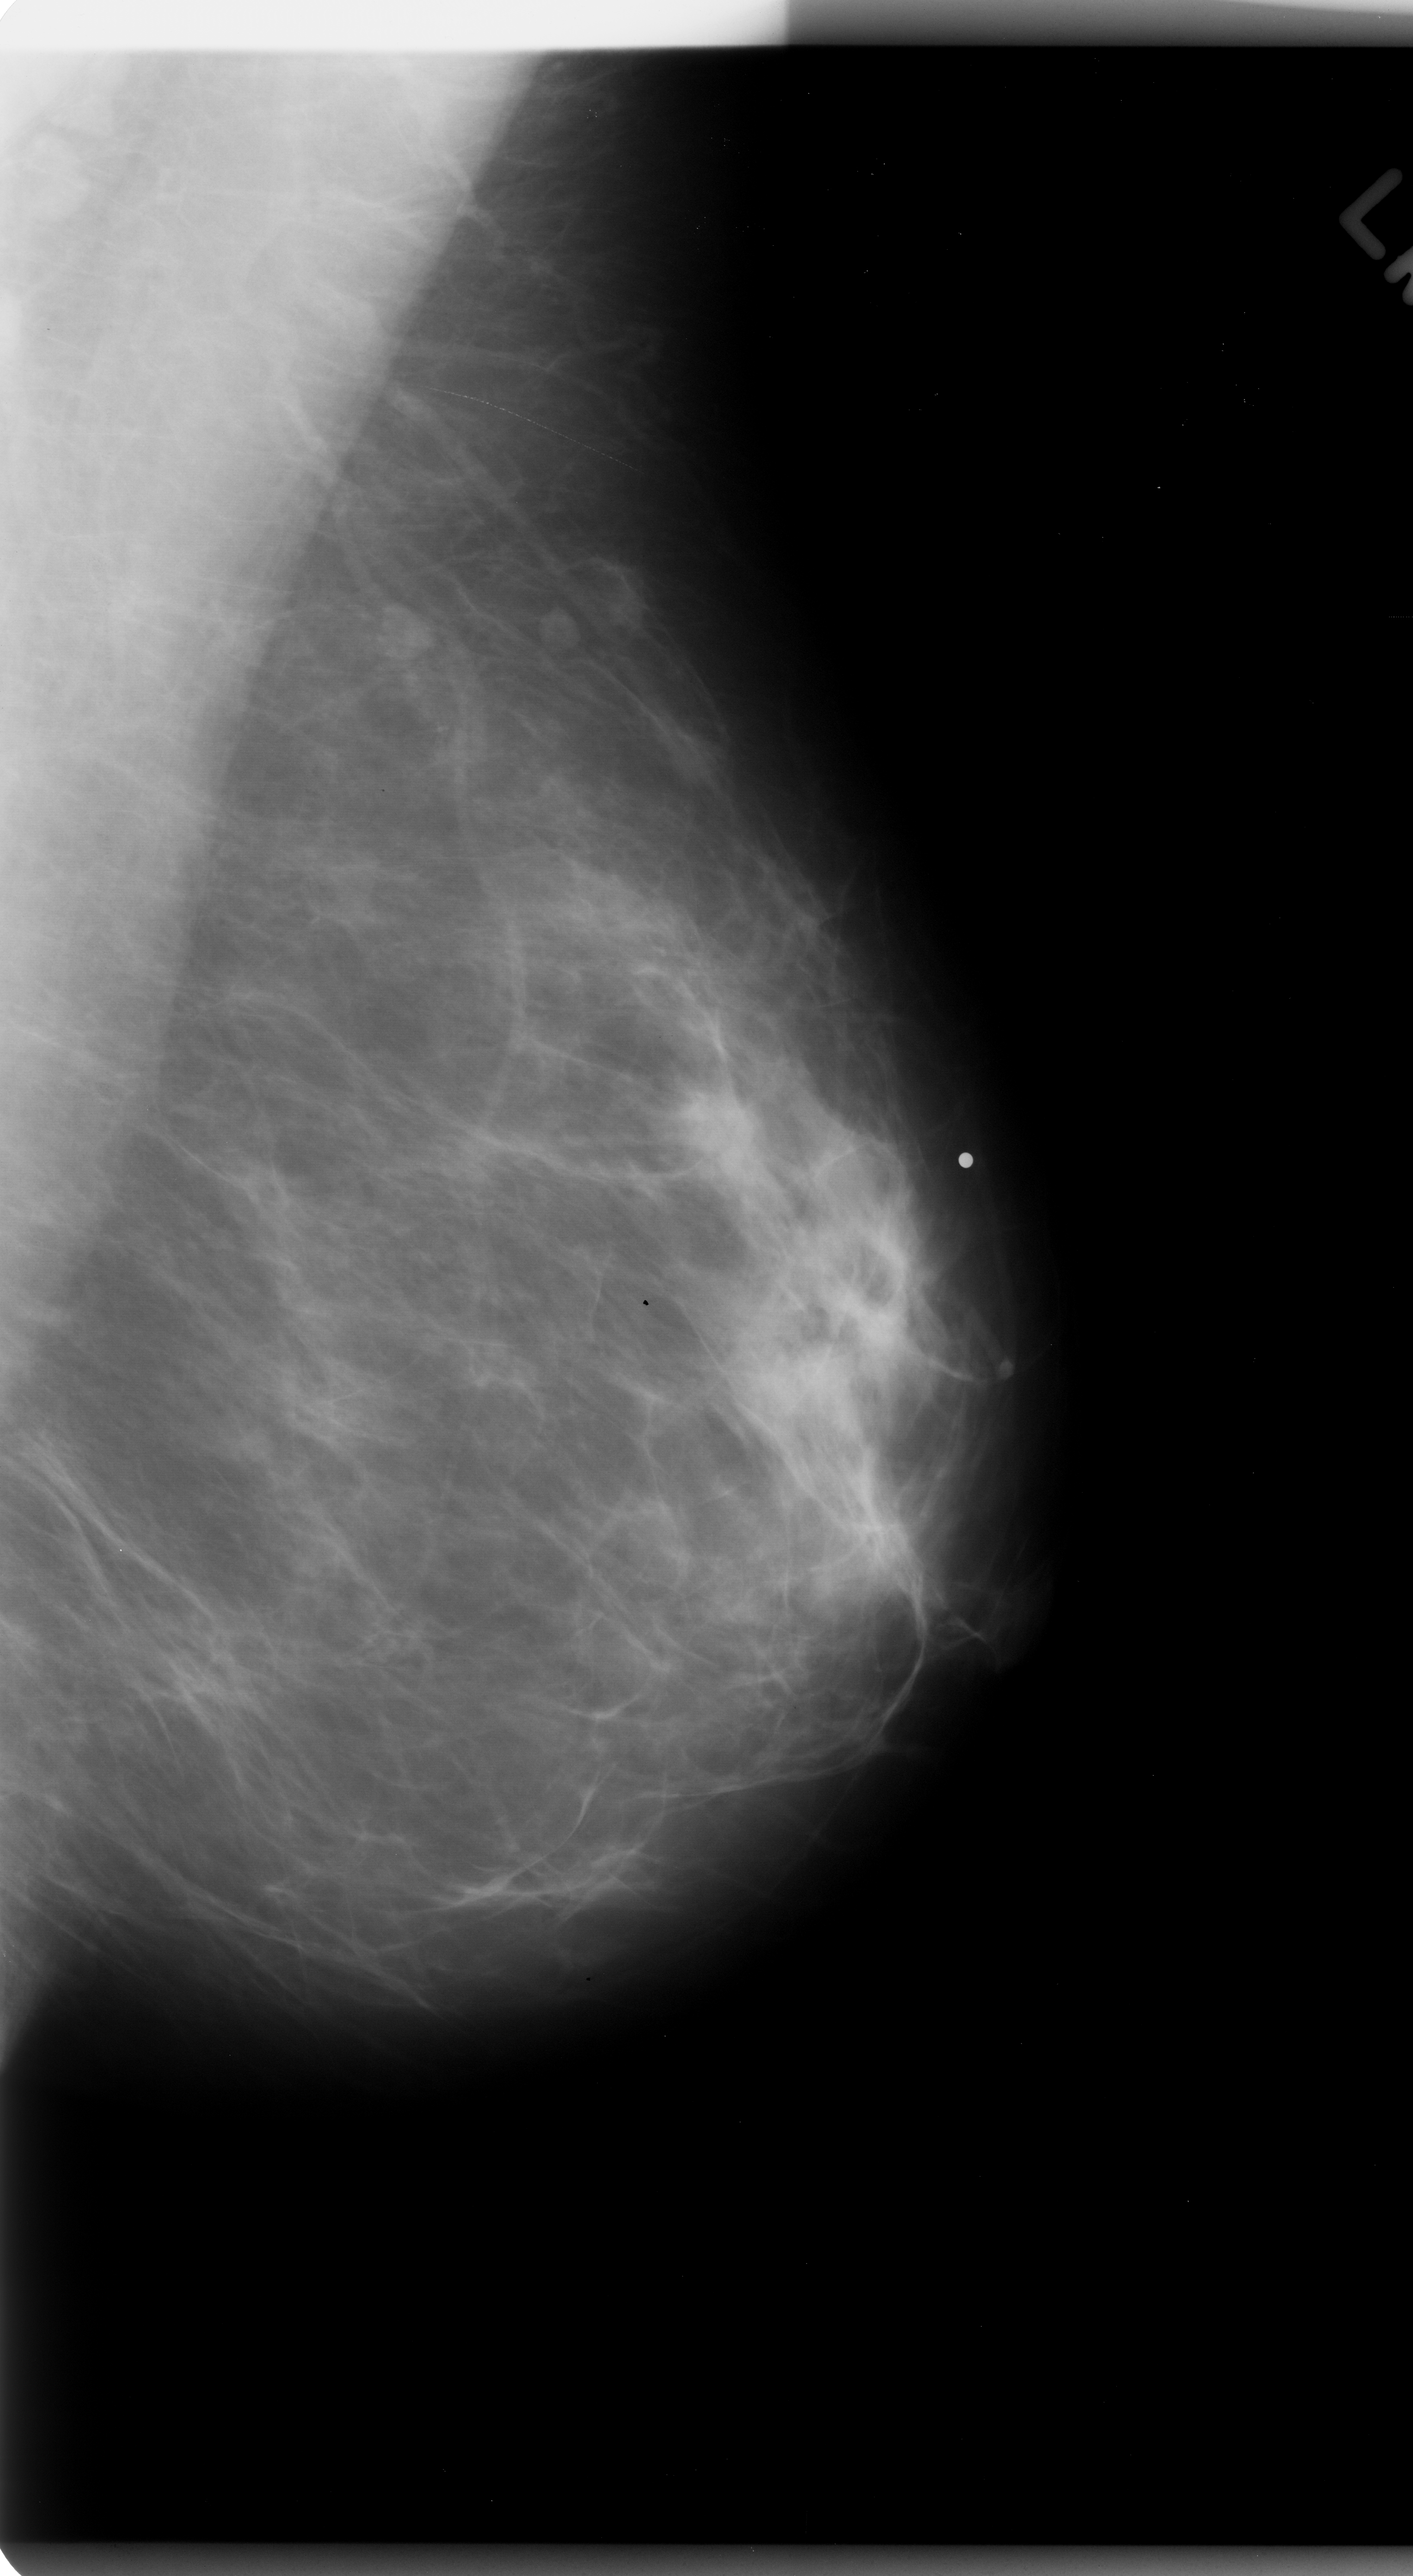
Mammogram (digitized film). Left breast. Mediolateral oblique (MLO) view. Breast composition: scattered fibroglandular densities (BI-RADS density category 2 of 4). 1413 × 2576 image matrix.
Expert-marked regions of interest on this image (one box per marked abnormality):
- mass, shape oval, margins spiculated; BI-RADS assessment category 5; pathology (as recorded): malignant: bounding box [x1, y1, x2, y2] px = [657, 1074, 768, 1198]